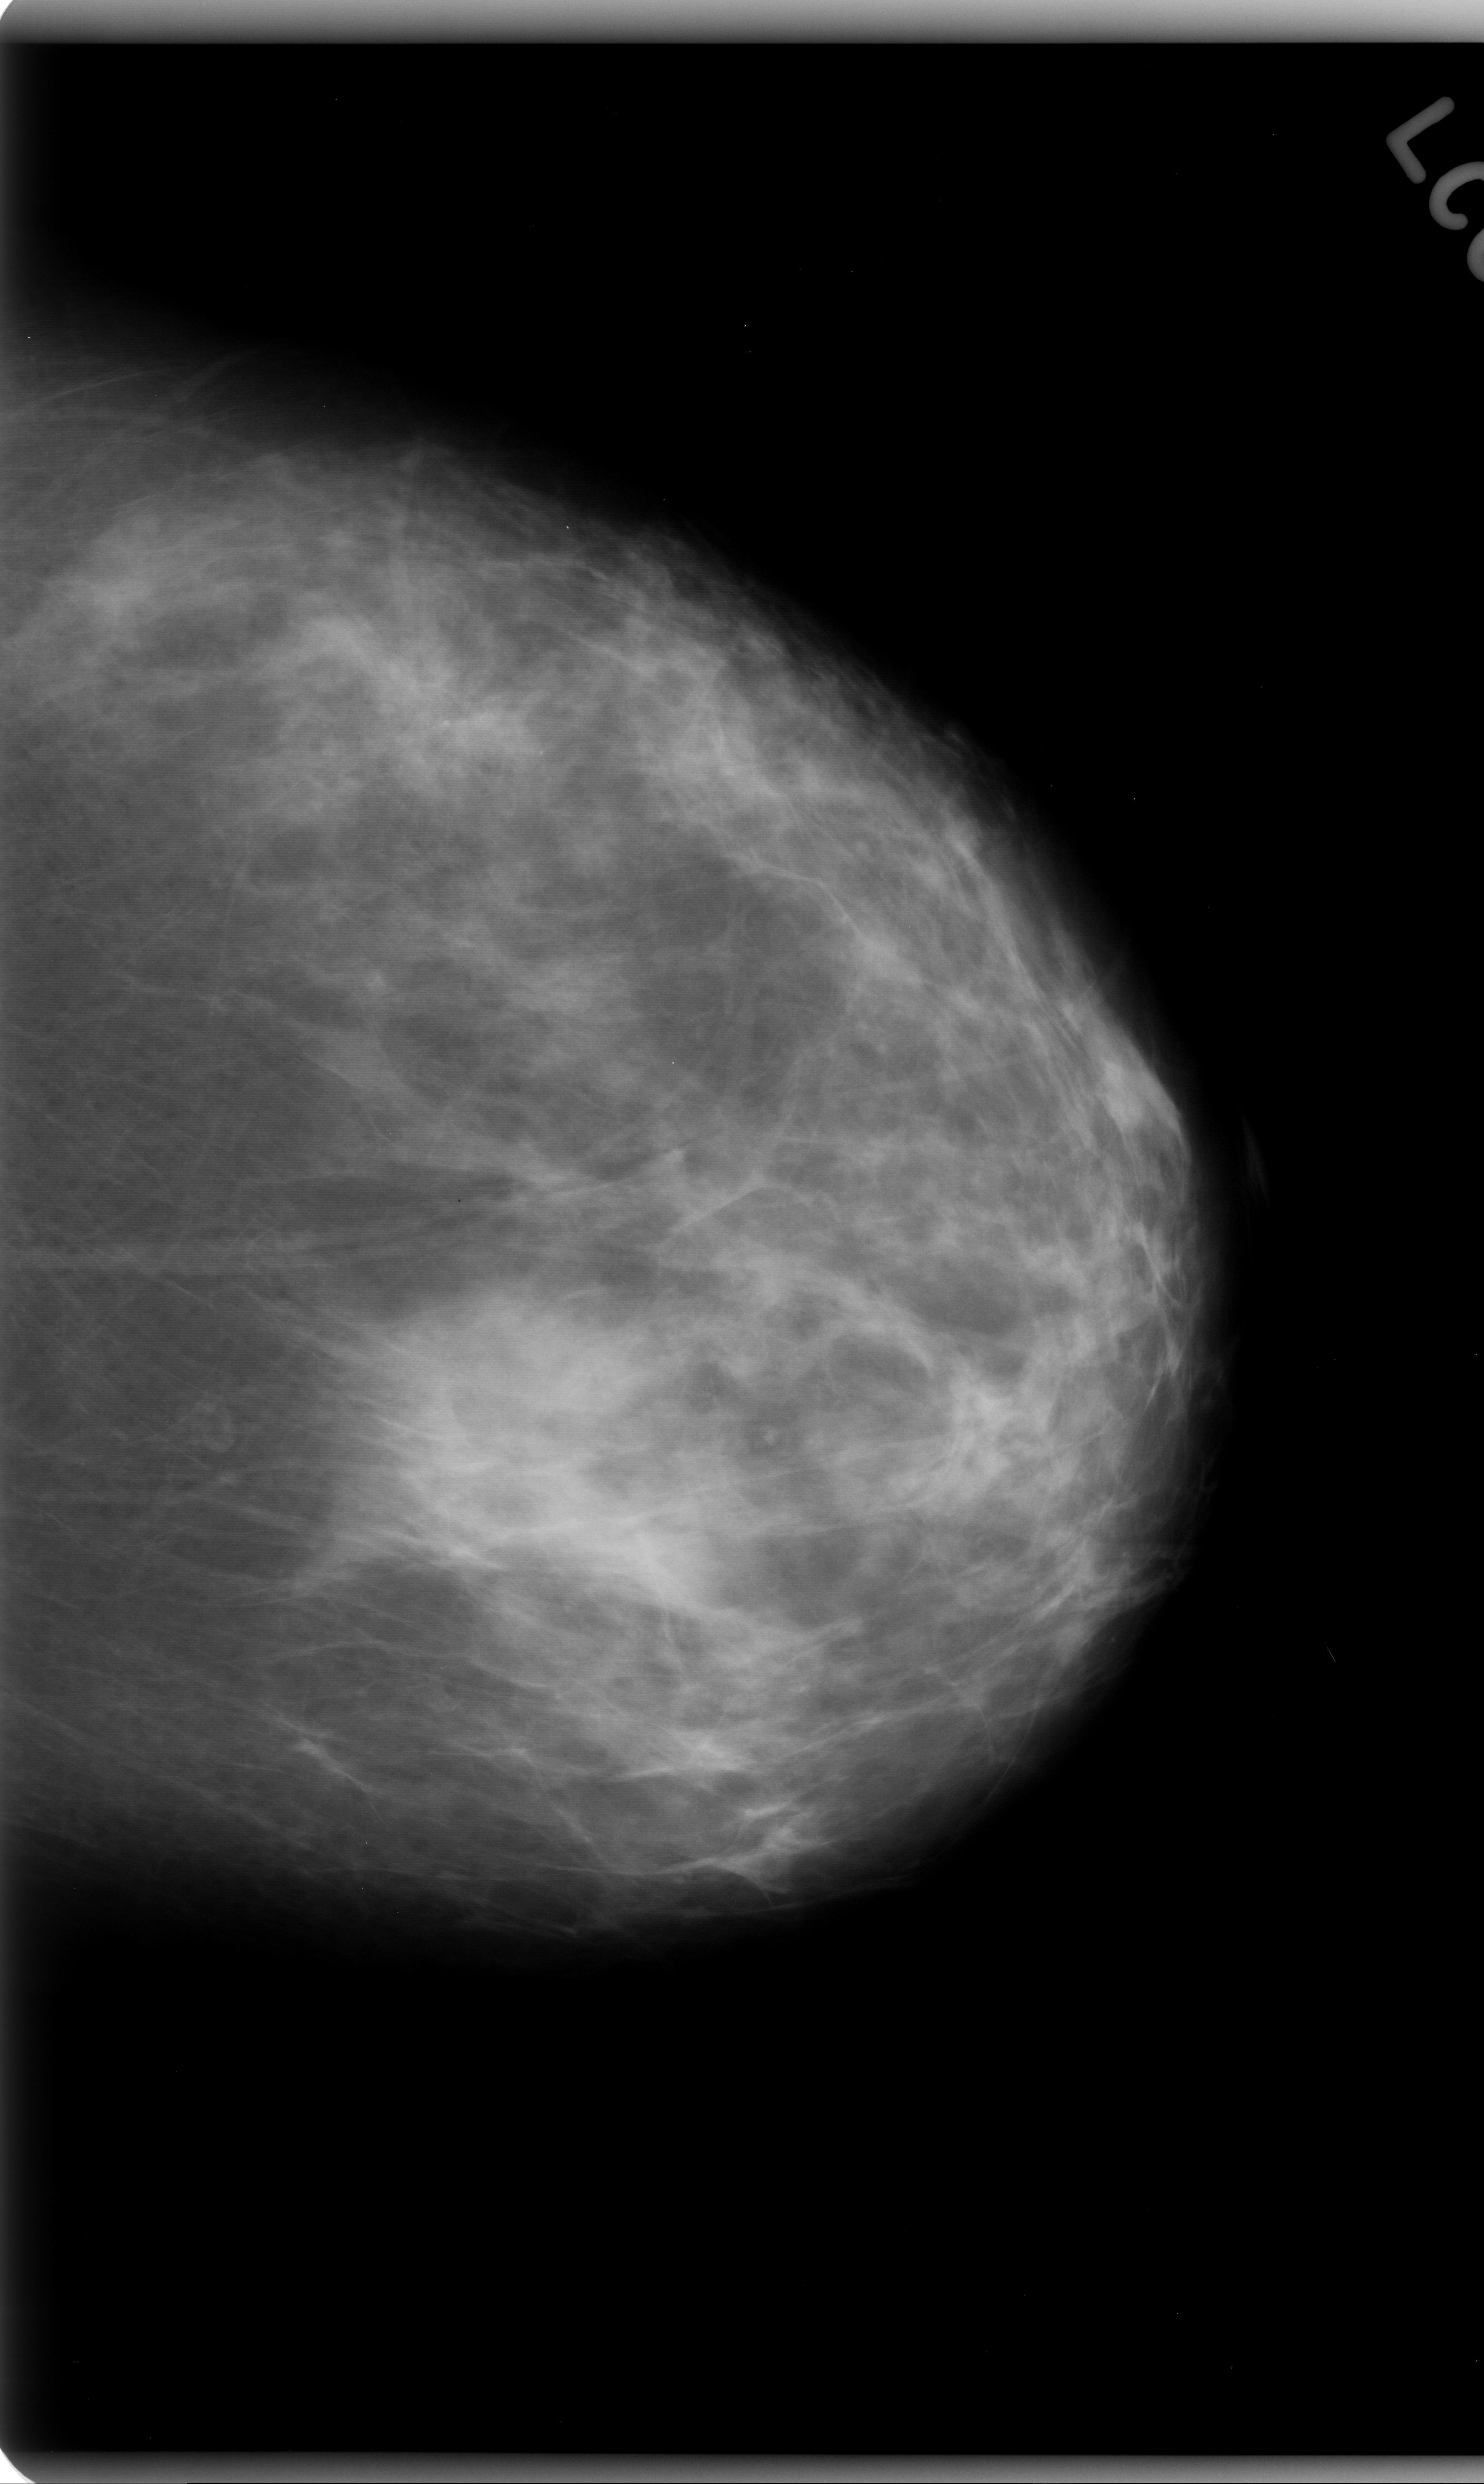
Mammogram (digitized film). Left breast. Craniocaudal (CC) view. Breast composition: scattered fibroglandular densities (BI-RADS density category 2 of 4). 1484 × 2484 image matrix.
Expert-marked regions of interest on this film, with their recorded descriptors:
- calcifications, morphology pleomorphic, distribution clustered; BI-RADS assessment category 4; pathology (as recorded): malignant: bounding box [x1, y1, x2, y2] px = [243, 521, 636, 867]